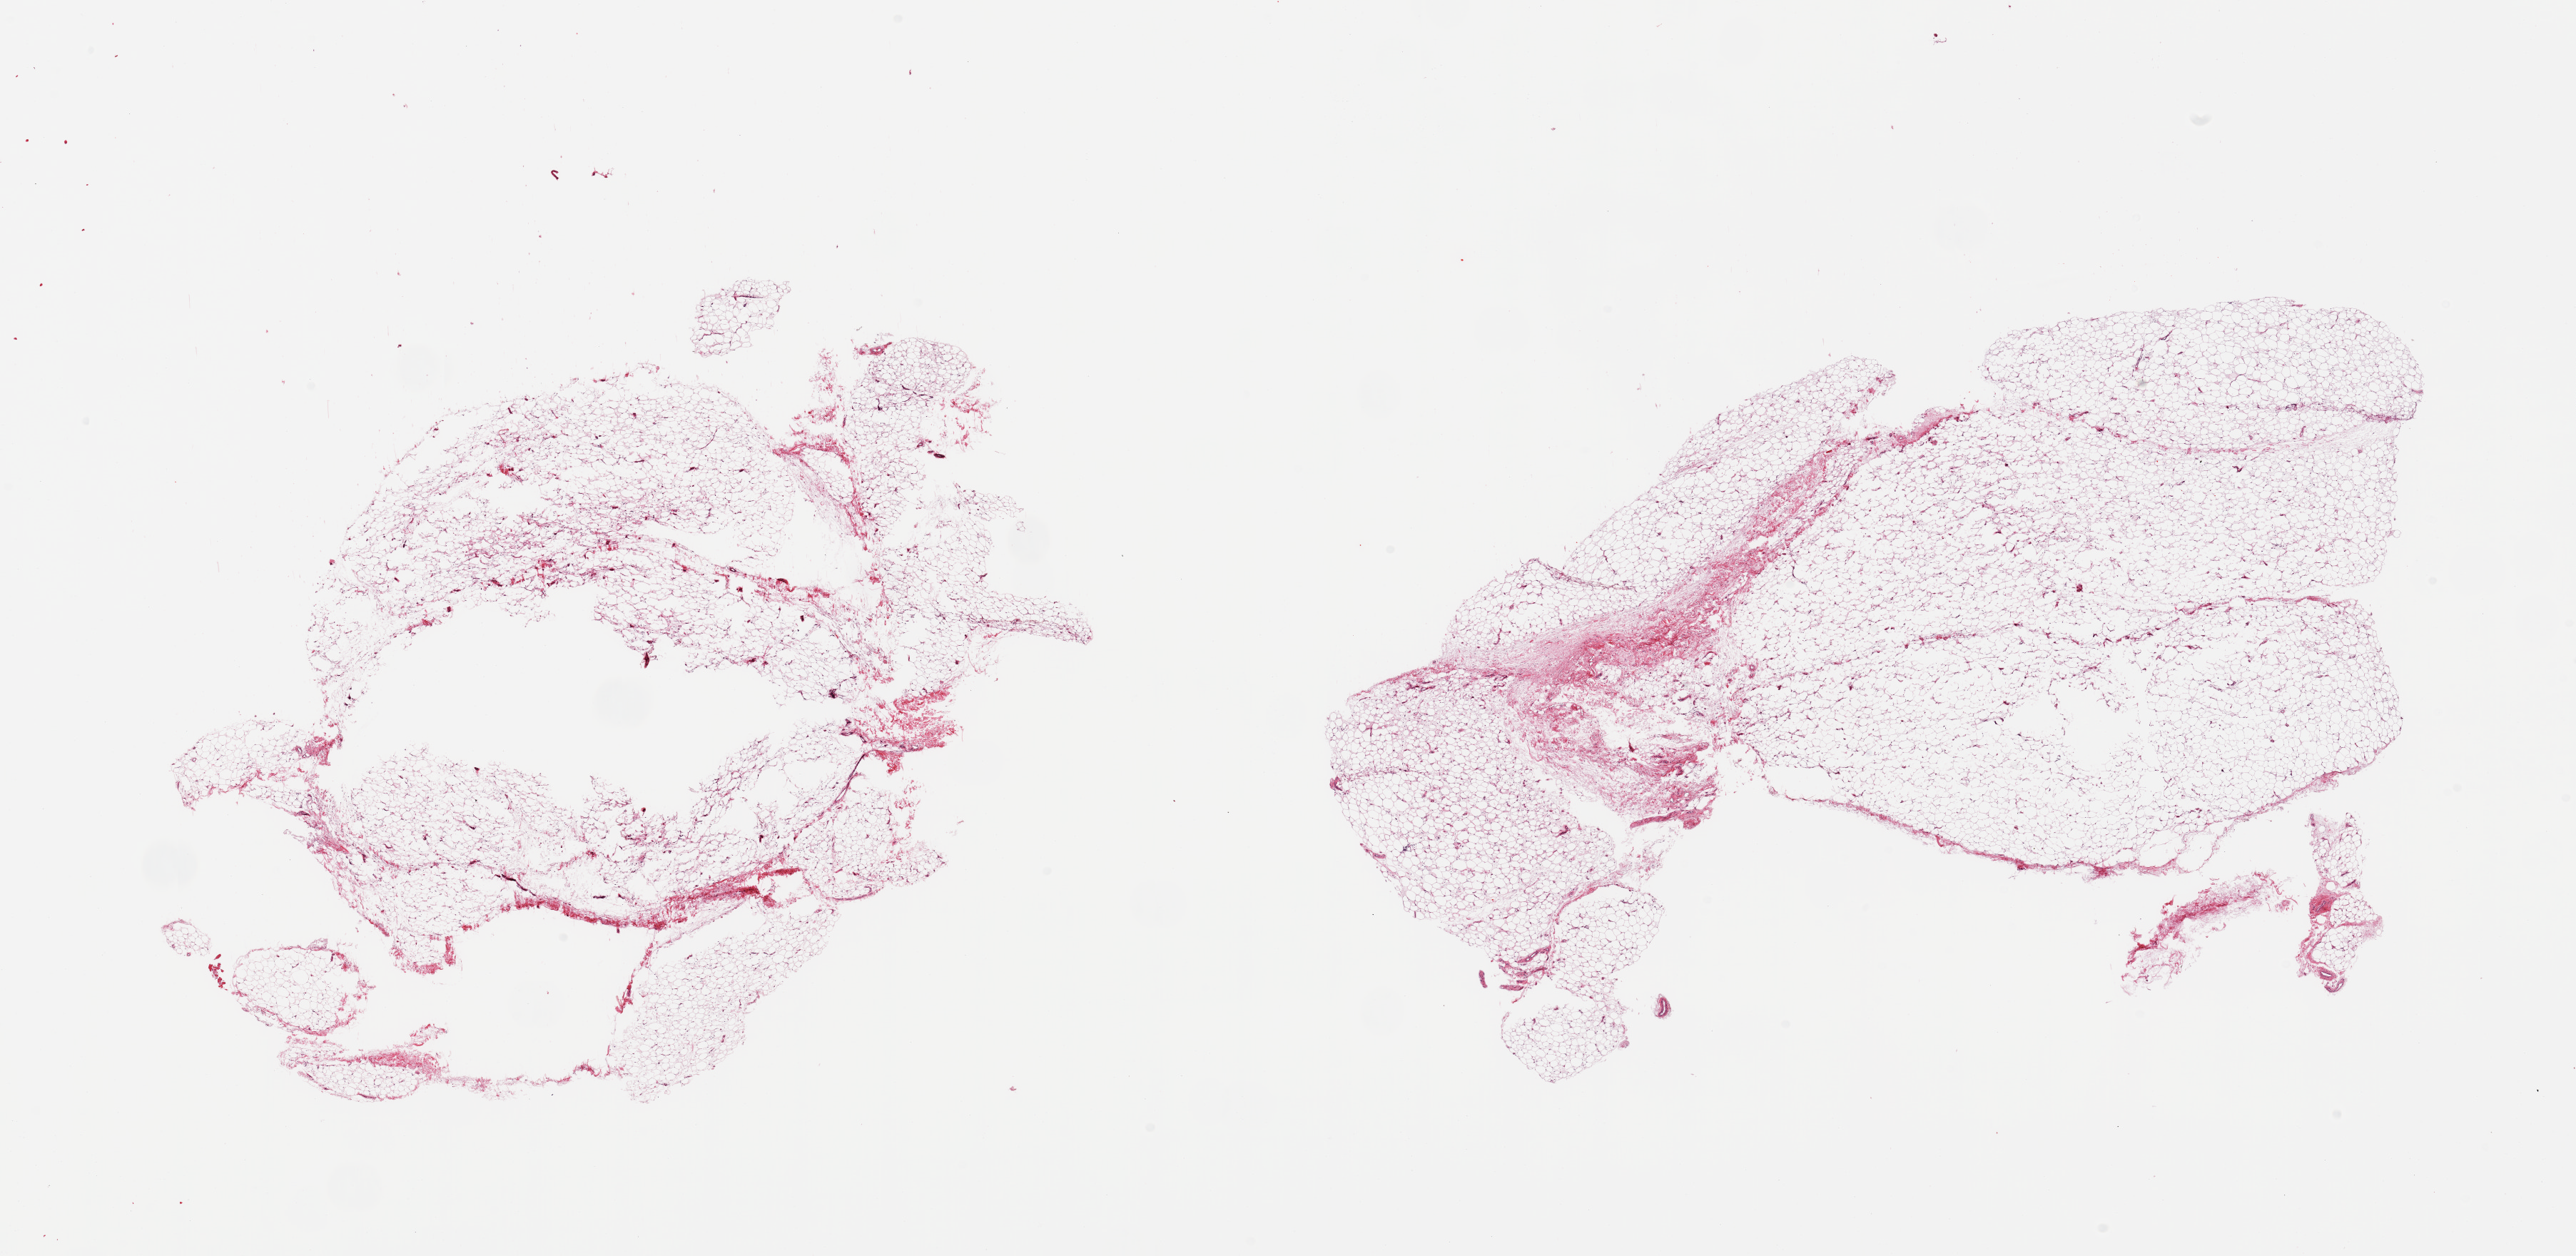
Digitized haematoxylin and eosin-stained section, brightfield, whole scanned area (about 28.5 x 13.9 mm, acquisition: 20x scan) shown as a low-resolution overview. PAXgene-fixed, paraffin-embedded tissue. Sampled site (target tissue): adipose tissue. Tissue donor sample.
Pathologist's review note for this sample: 2 pieces; large central defects.